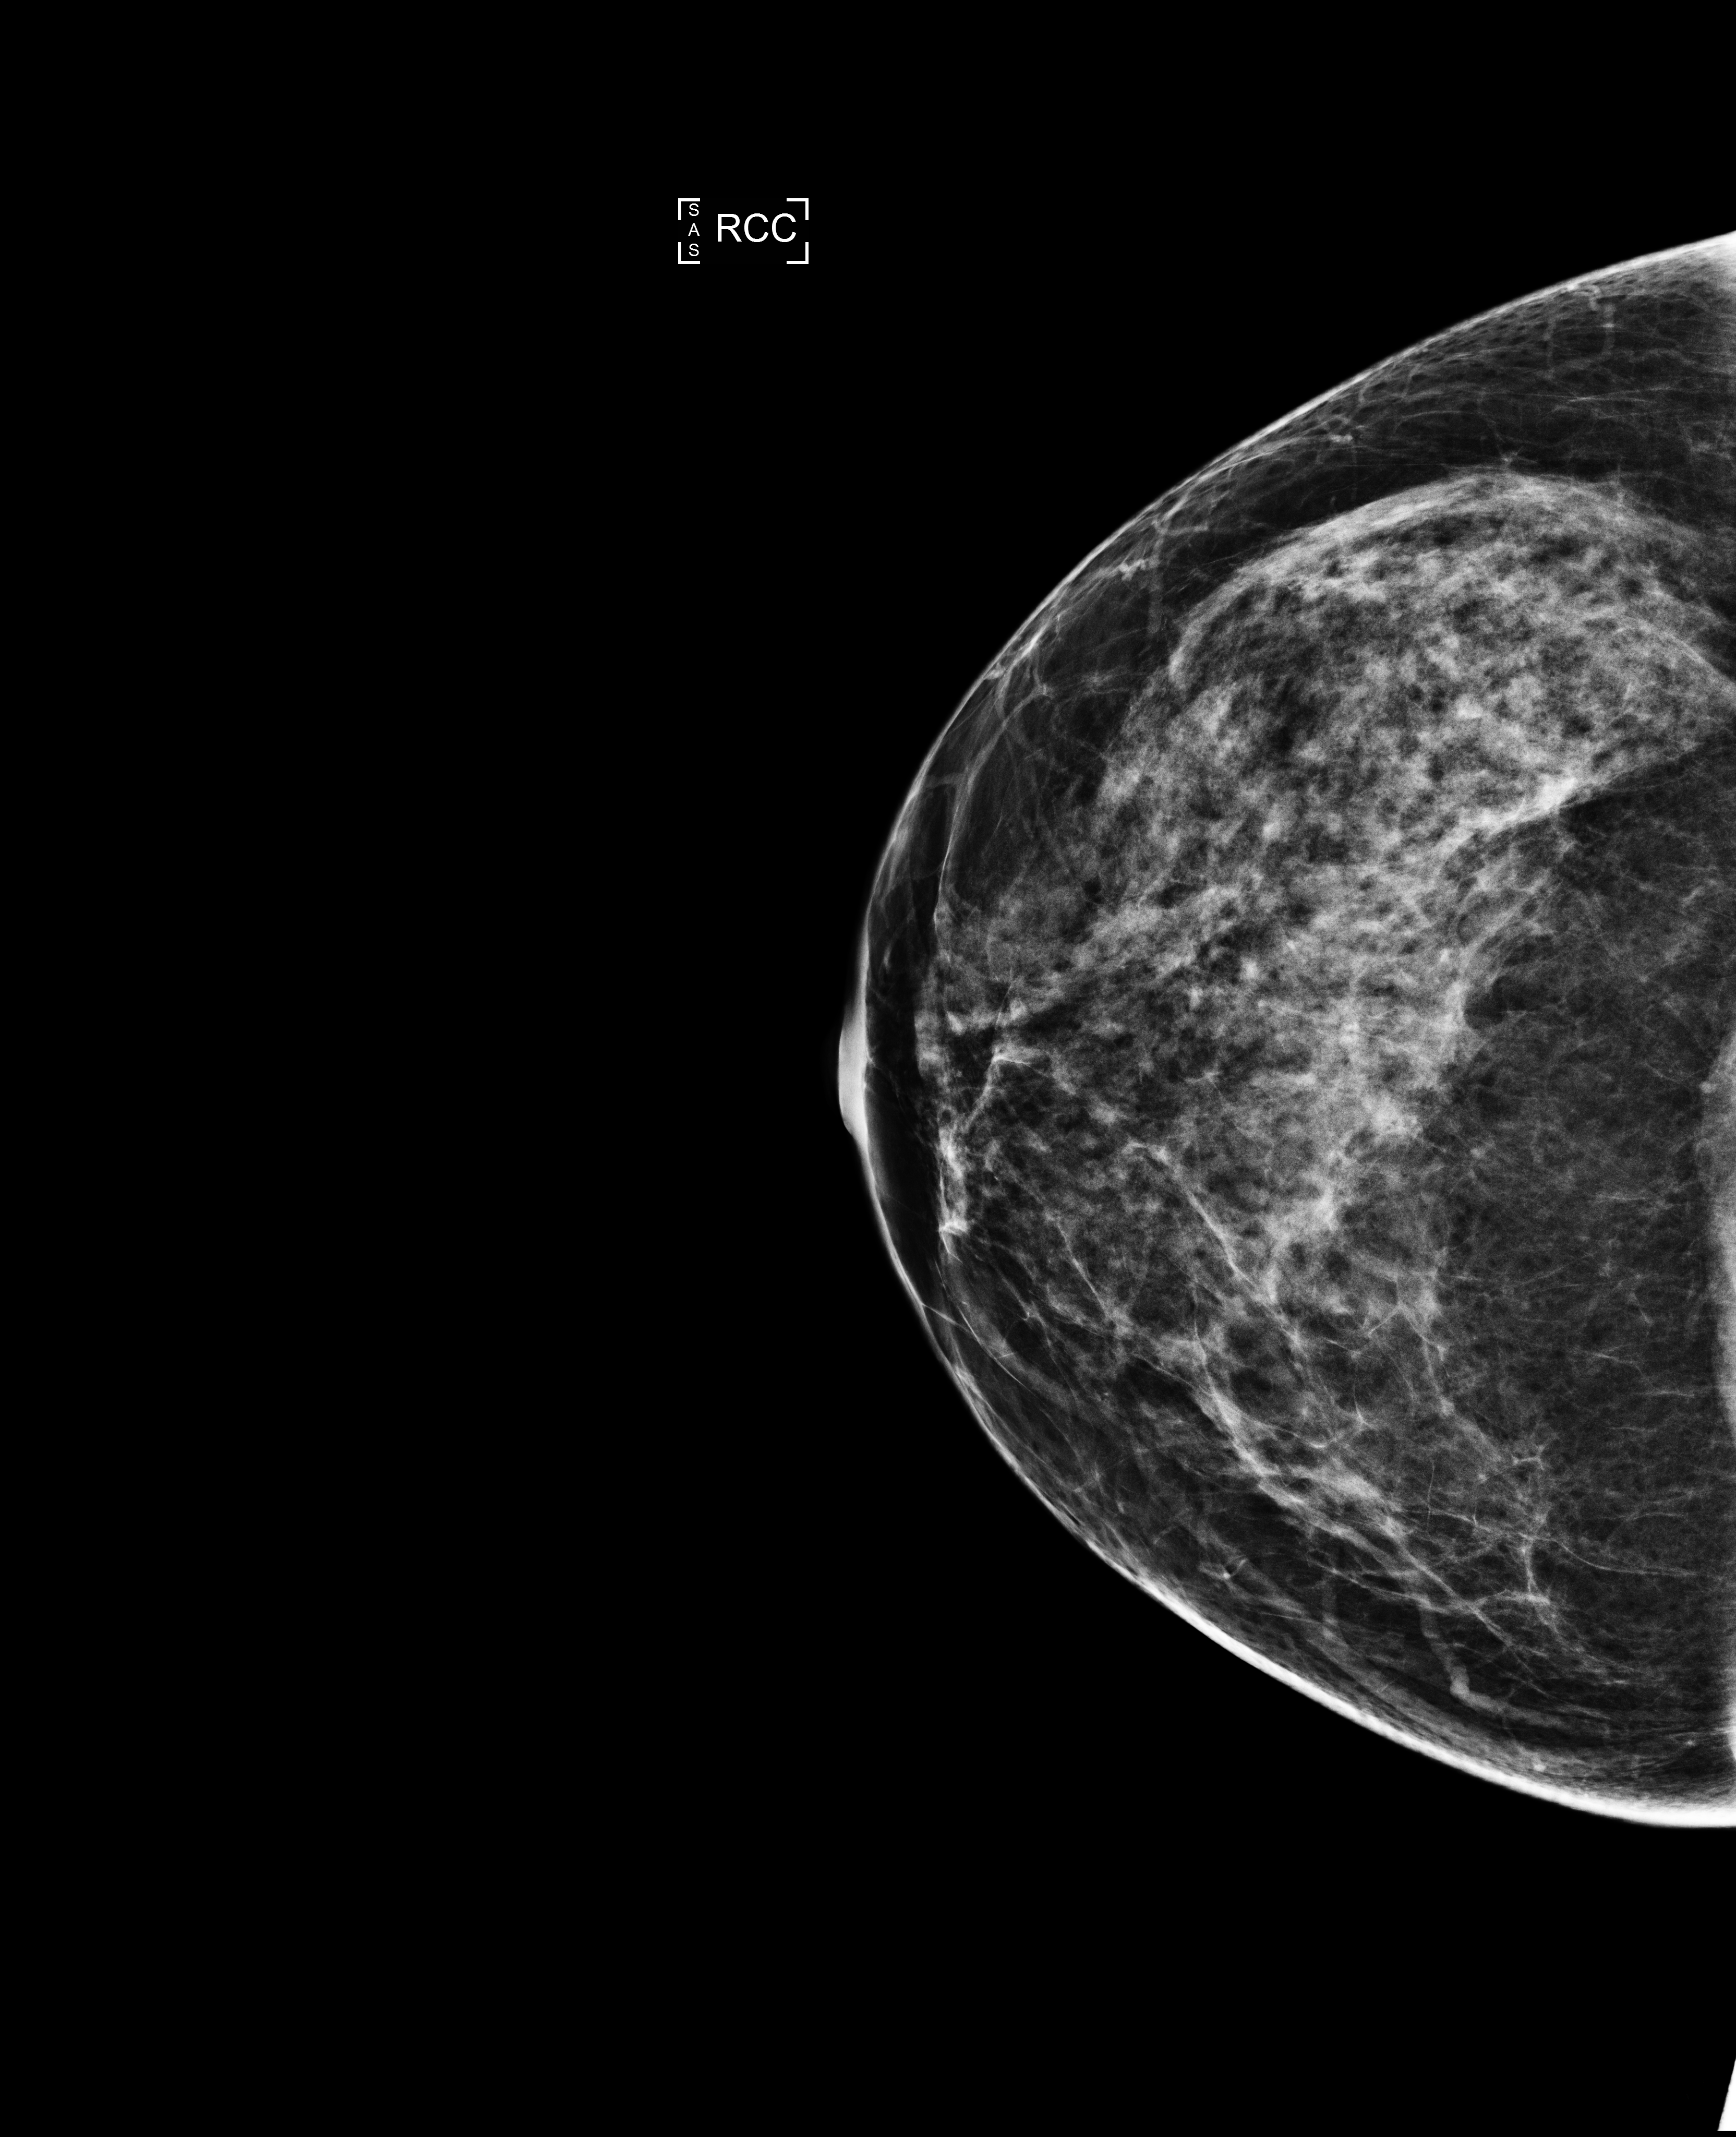
Annual screening mammography examination. Patient aged 45 years (female).
Image type: full-field digital mammogram. Breast: right. Projection: cranio-caudal projection.